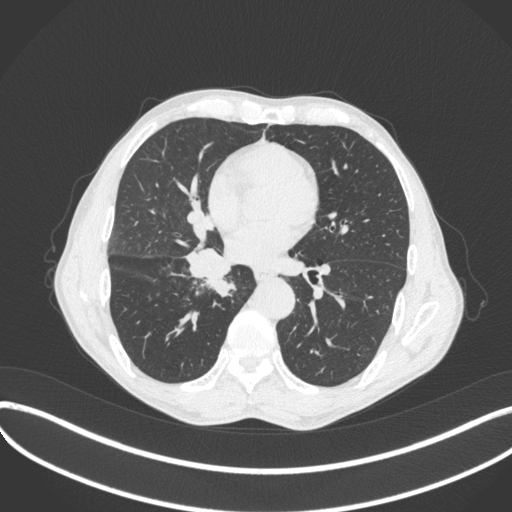
Chest CT, one axial slice. Slice 201 of 481 in the series (ordered by position). Reconstruction kernel B31f. Lung window (W 1500 / L -600 HU). 1 mm slice thickness. 512 × 512 image matrix, field of view 400 × 400 mm. Male patient, age 65 years. From the clinical record (not read from this slice): clinical TNM (as recorded): T2a N0 M0.
Structures marked on this image (bounding box drawn by a radiologist):
- lung tumour (recorded histology: squamous cell carcinoma): bounding box (x1, y1, x2, y2) in pixels: (180, 249, 236, 297)